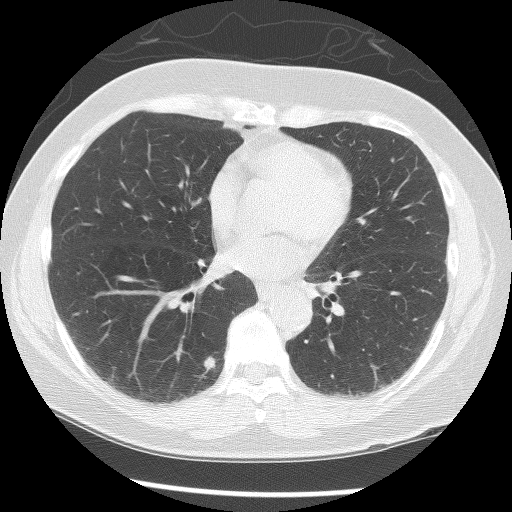
Low-dose screening chest CT, axial slice; baseline screening round; lung window (W 1500 / L -600 HU); lung (sharp) reconstruction kernel (BONE); slice 67 of 125 in the series; 512 × 512 image matrix, field of view 331 × 331 mm. Female participant, aged 56 years at enrolment. Current smoker at enrolment.
• Lesion marked by an expert reader, bounding box <189,347,231,388> (left, top, right, bottom; pixels).
• Reader record for this screening exam (exam-level; its link to the box is not recorded): non-calcified nodule or mass ≥4 mm, right lower lobe, 8 × 7 mm, smooth margins, soft tissue attenuation.
• Participant outcome: lung cancer diagnosed 167 days after this screen — adenocarcinoma, NOS, right lower lobe, poorly differentiated (G3), stage IA (AJCC 6th edition), 12 mm at pathology.